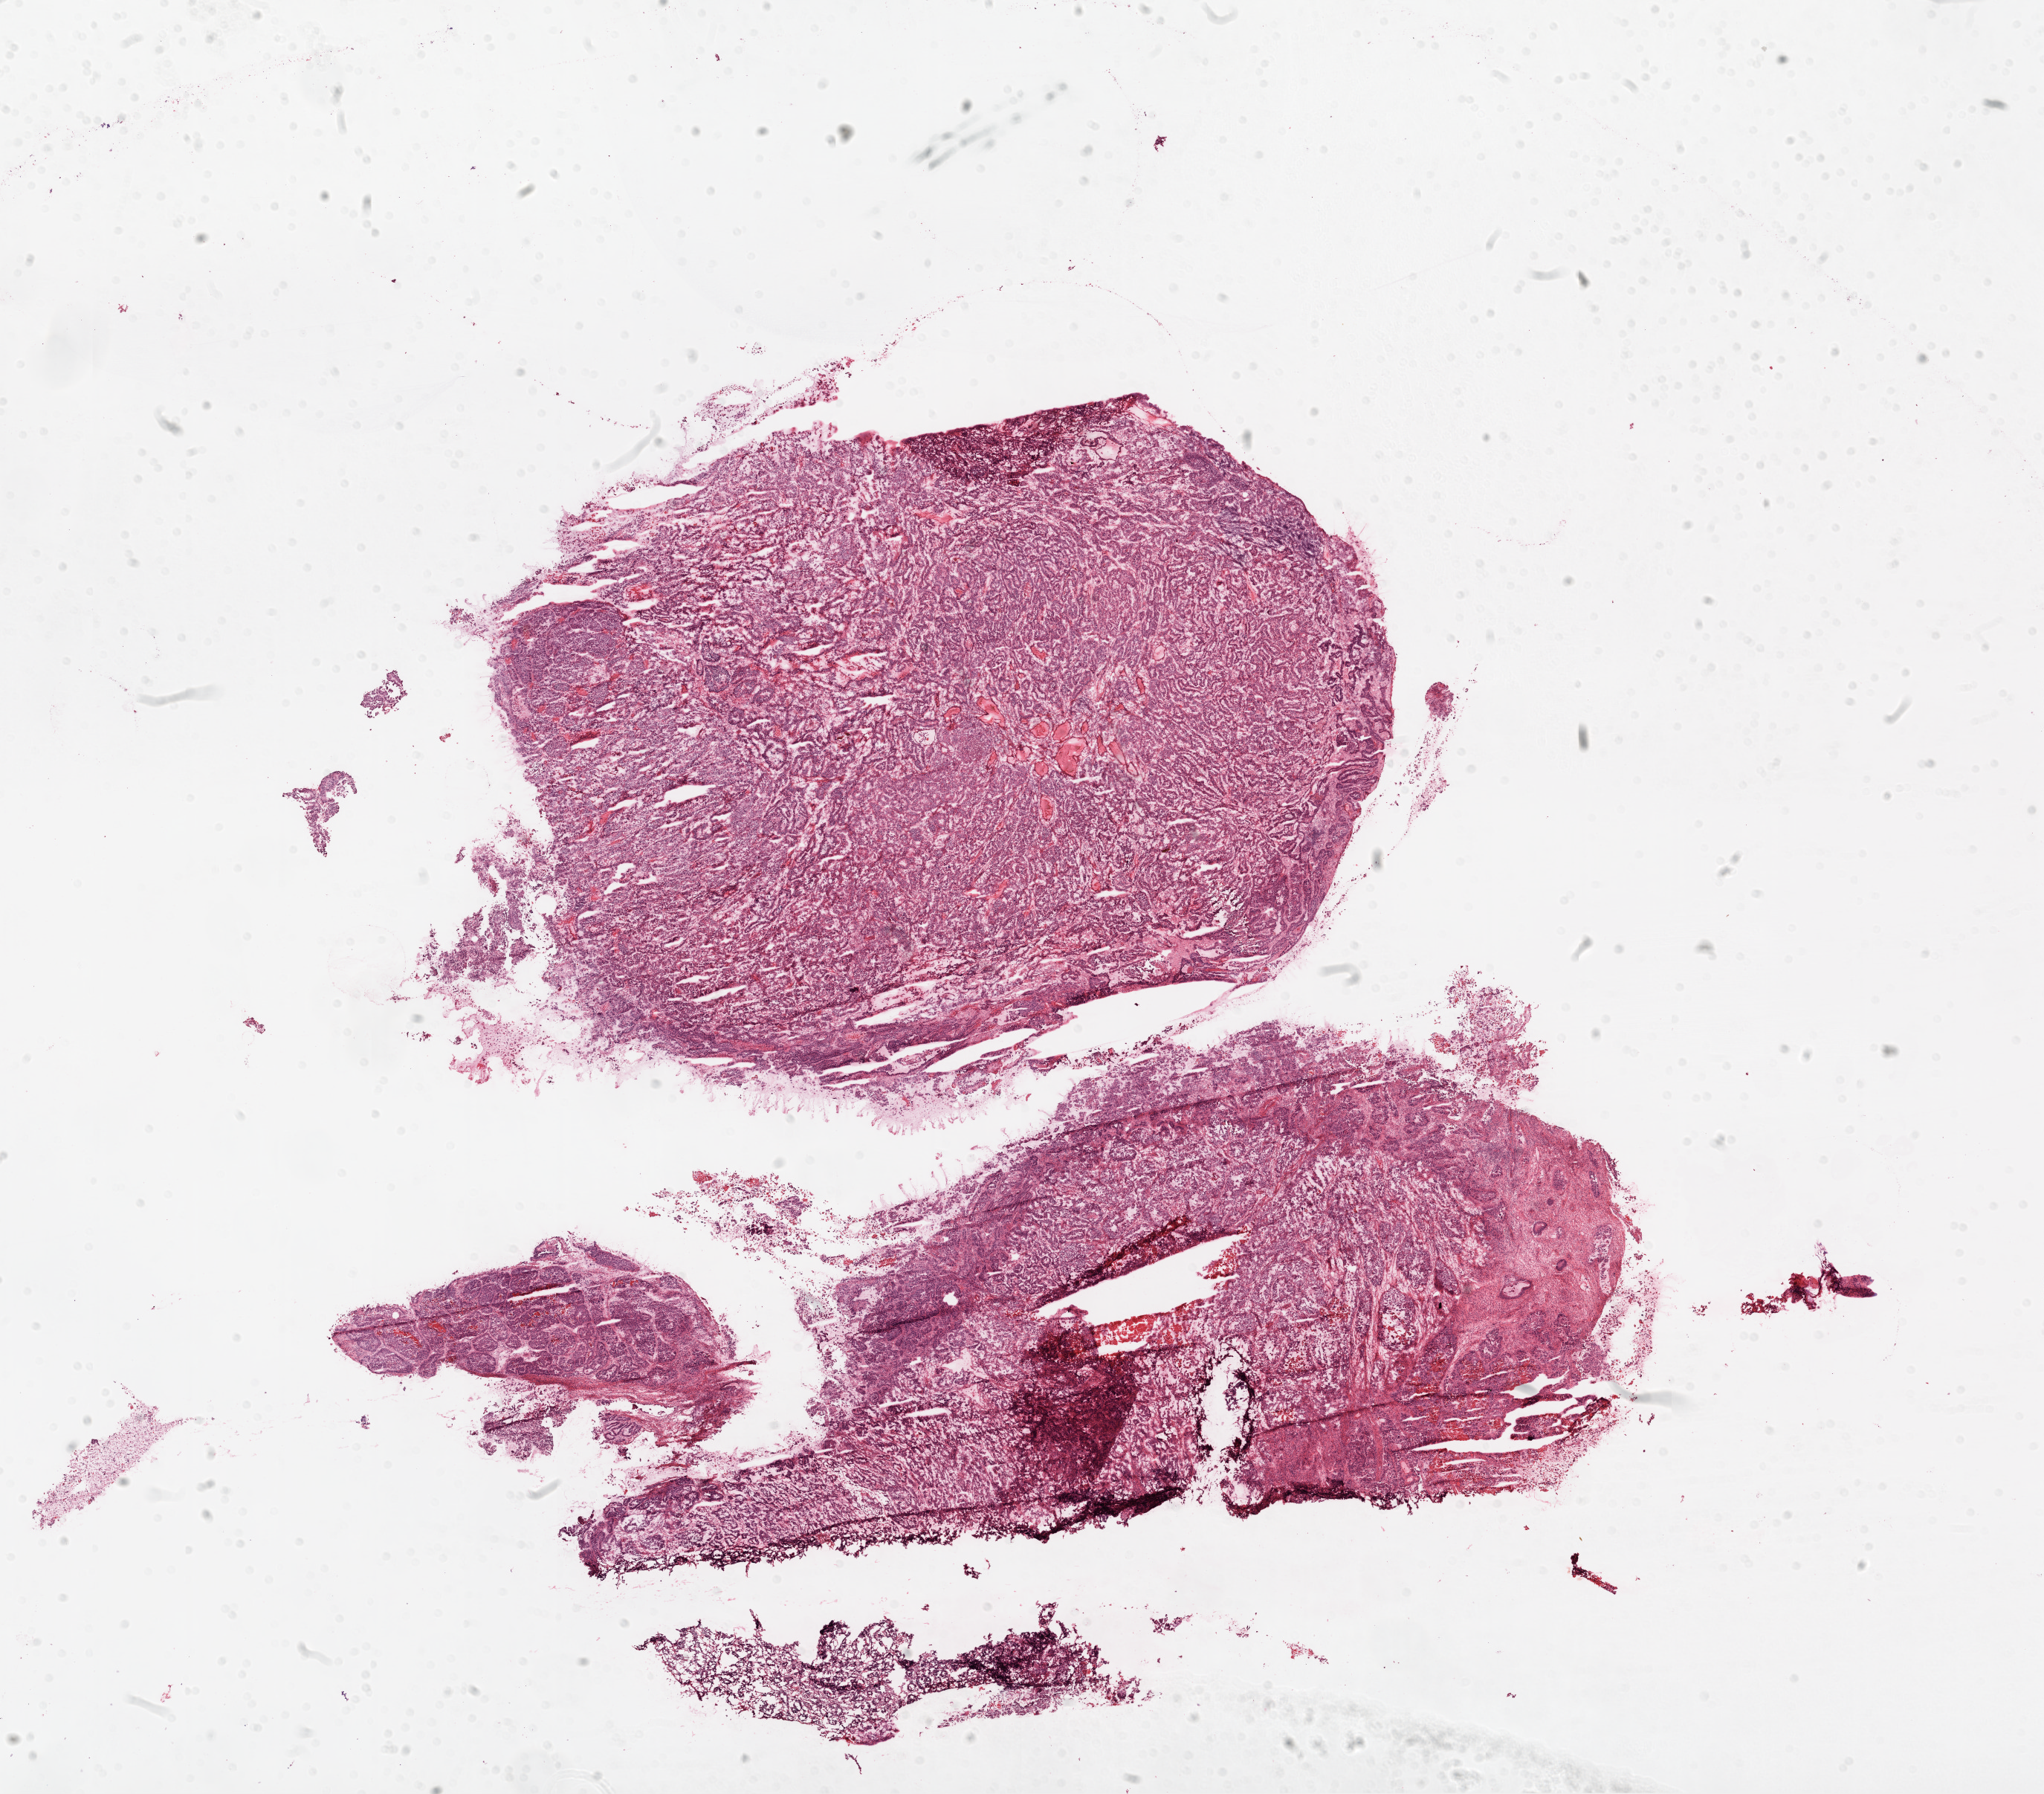
Digitized H&E tissue section (whole slide), shown as a low-resolution overview of the whole scanned area (about 22.1 x 19.4 mm); frozen section from the top of the tissue portion; sample: primary tumour, ovary. Patient: female, age at initial diagnosis 61 years. Histologic grade: G3 (poorly differentiated). Slide review estimates, as recorded: tumour cells 80%, tumour nuclei 75%, normal cells 3%, stromal cells 3%, necrosis 14%.
Histologic diagnosis: Serous cystadenocarcinoma, NOS. FIGO stage: IV.